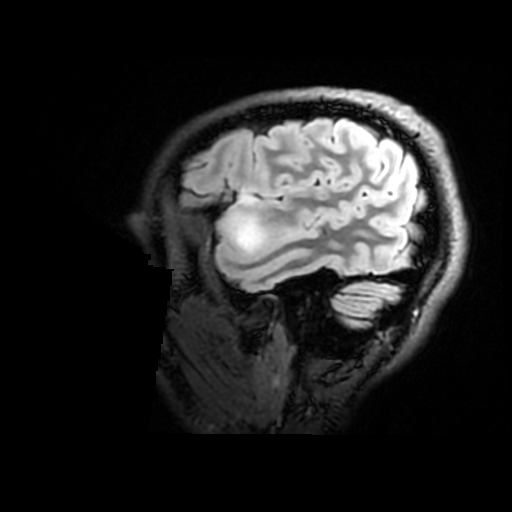
Brain MRI from a brain-tumour surgery series, one sagittal slice. Position 140 of 176 along the scan axis. T2 FLAIR. 512 × 512 image matrix. Case-level facts recorded for this patient, not image findings: histopathology: Astrocytoma; WHO grade: 2.
Structures marked on this image (manually delineated by an expert):
- tumour: box from (x=233, y=192) to (x=258, y=252) px